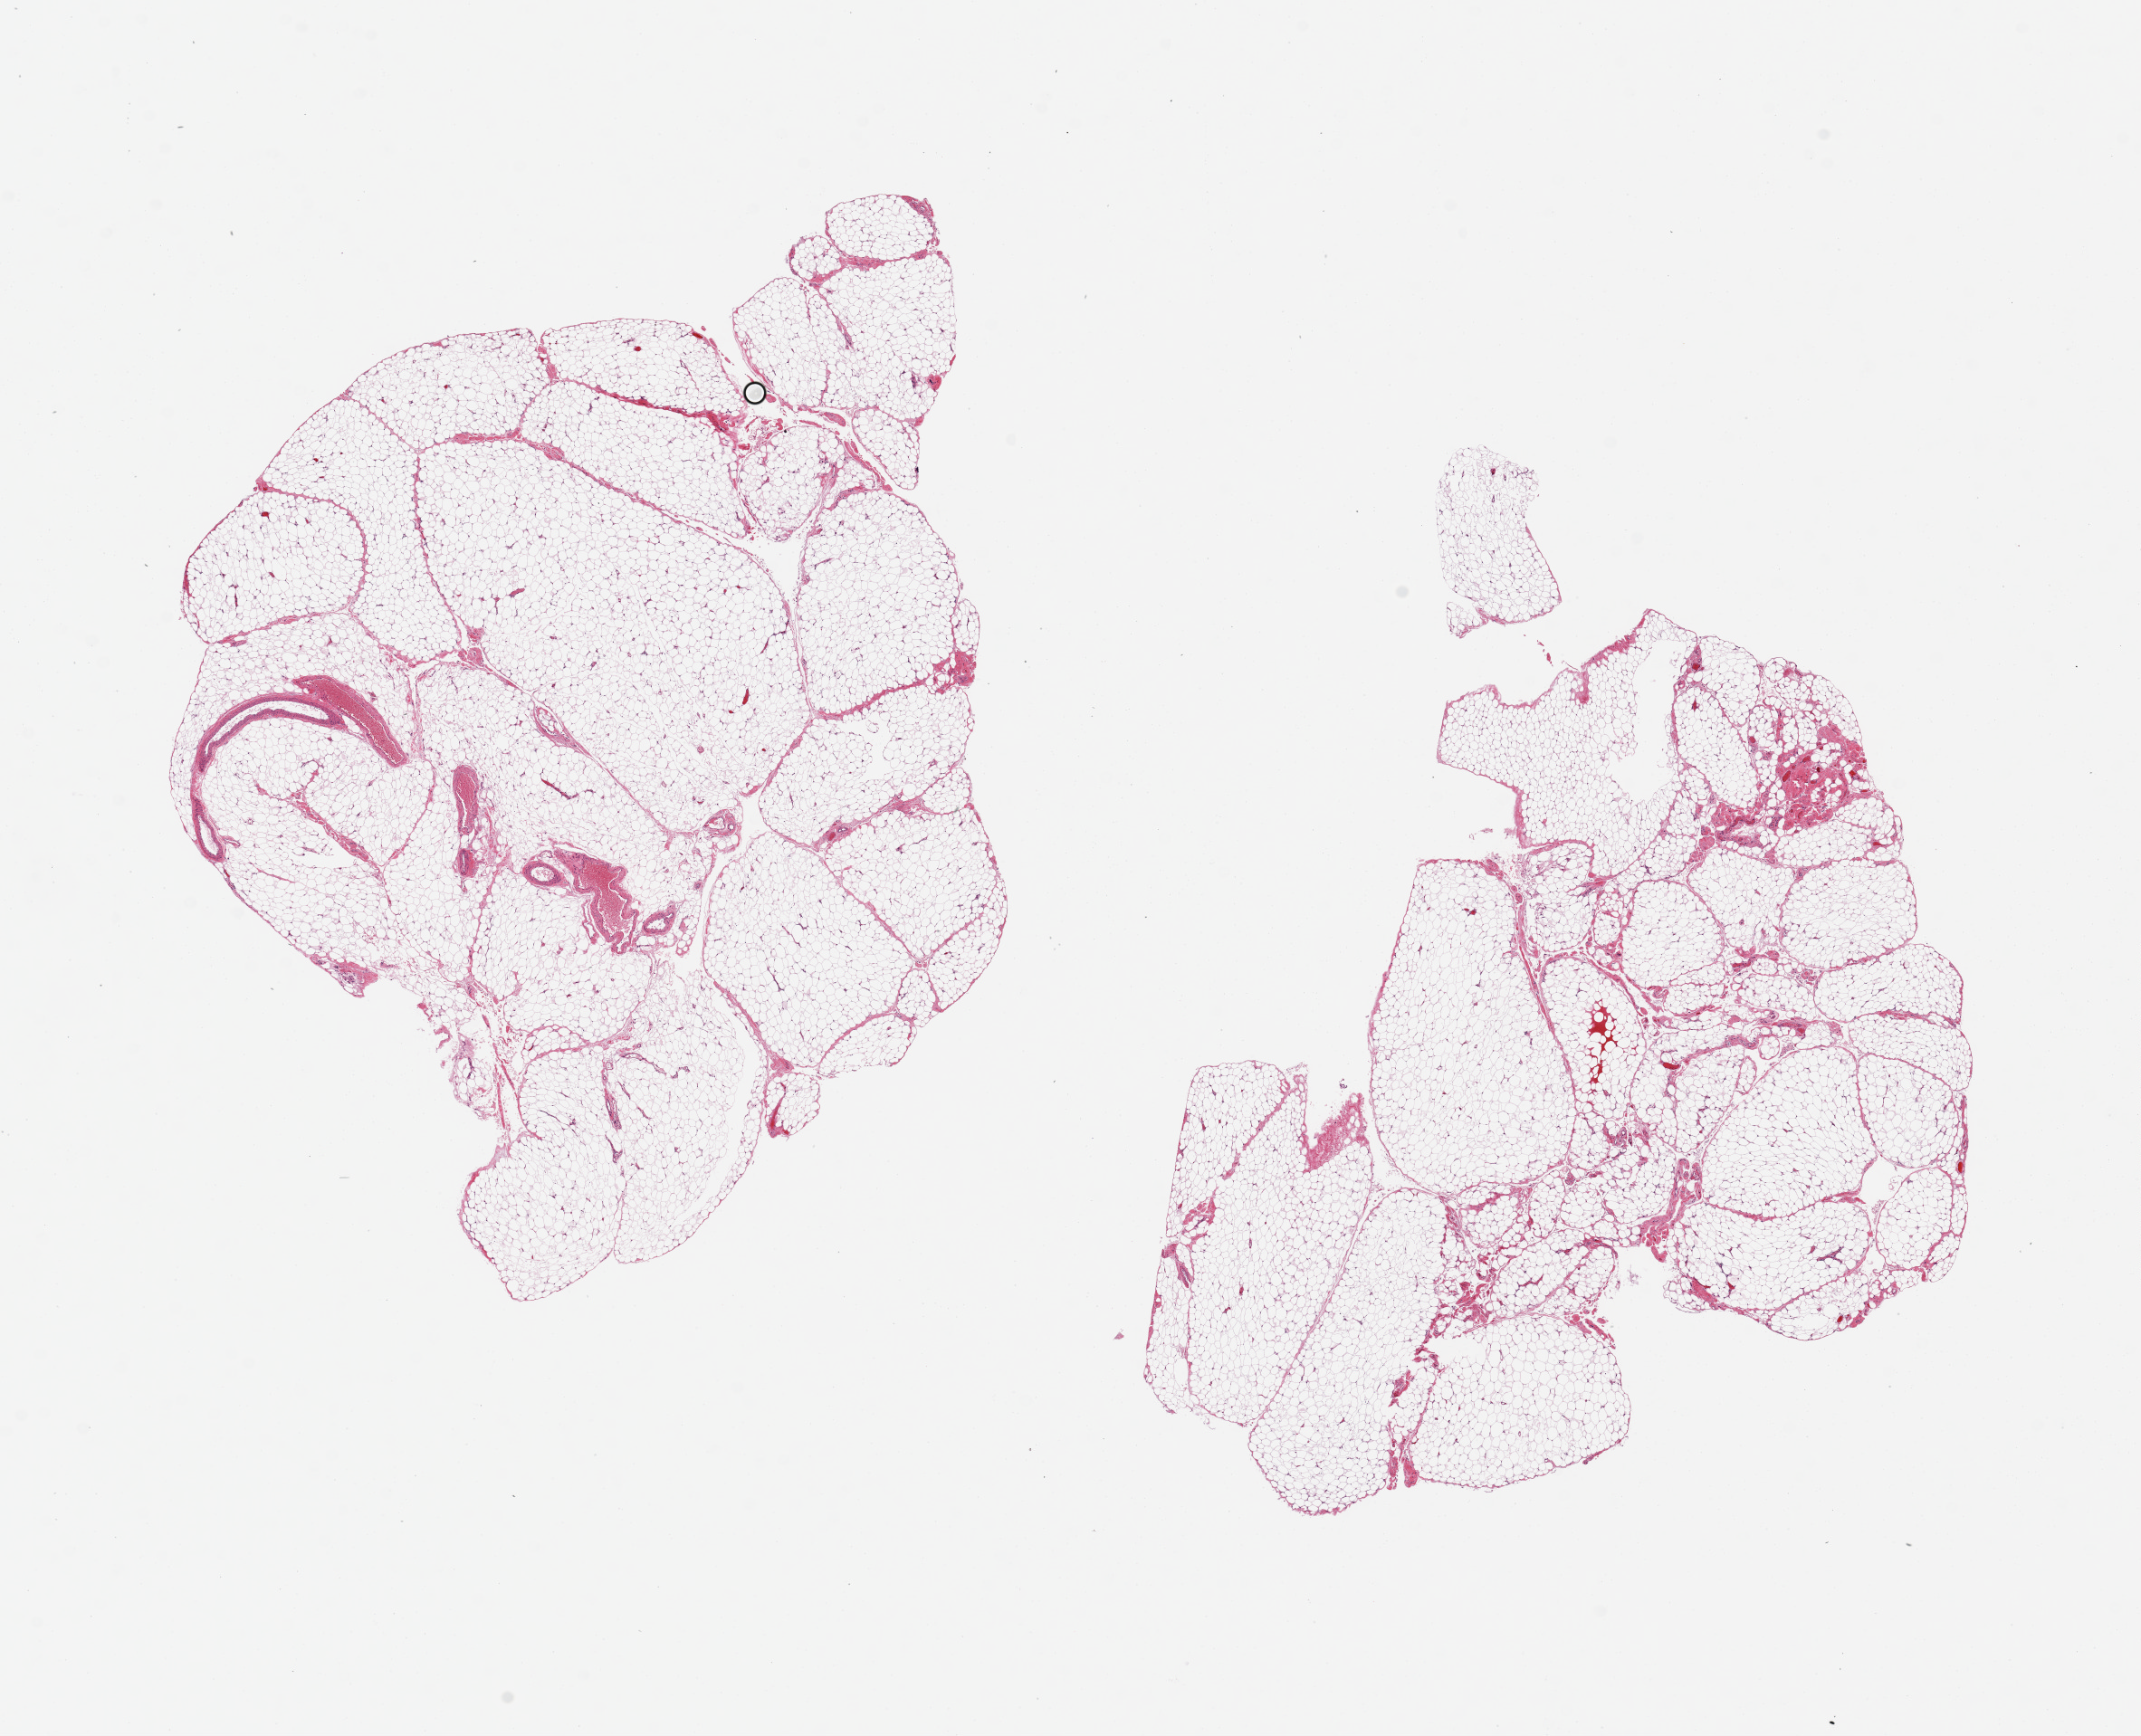
Haematoxylin and eosin whole-slide image, whole scanned area (about 18.7 x 15.2 mm, slide scanned at 20x) shown as a low-resolution overview. PAXgene-fixed, paraffin-embedded tissue. Sampled site (target tissue): omentum. Donor tissue sample. Donor: male.
Review note (as recorded): 2 pieces, 10x7 & 9x7mm; well fixed, no artifacts.